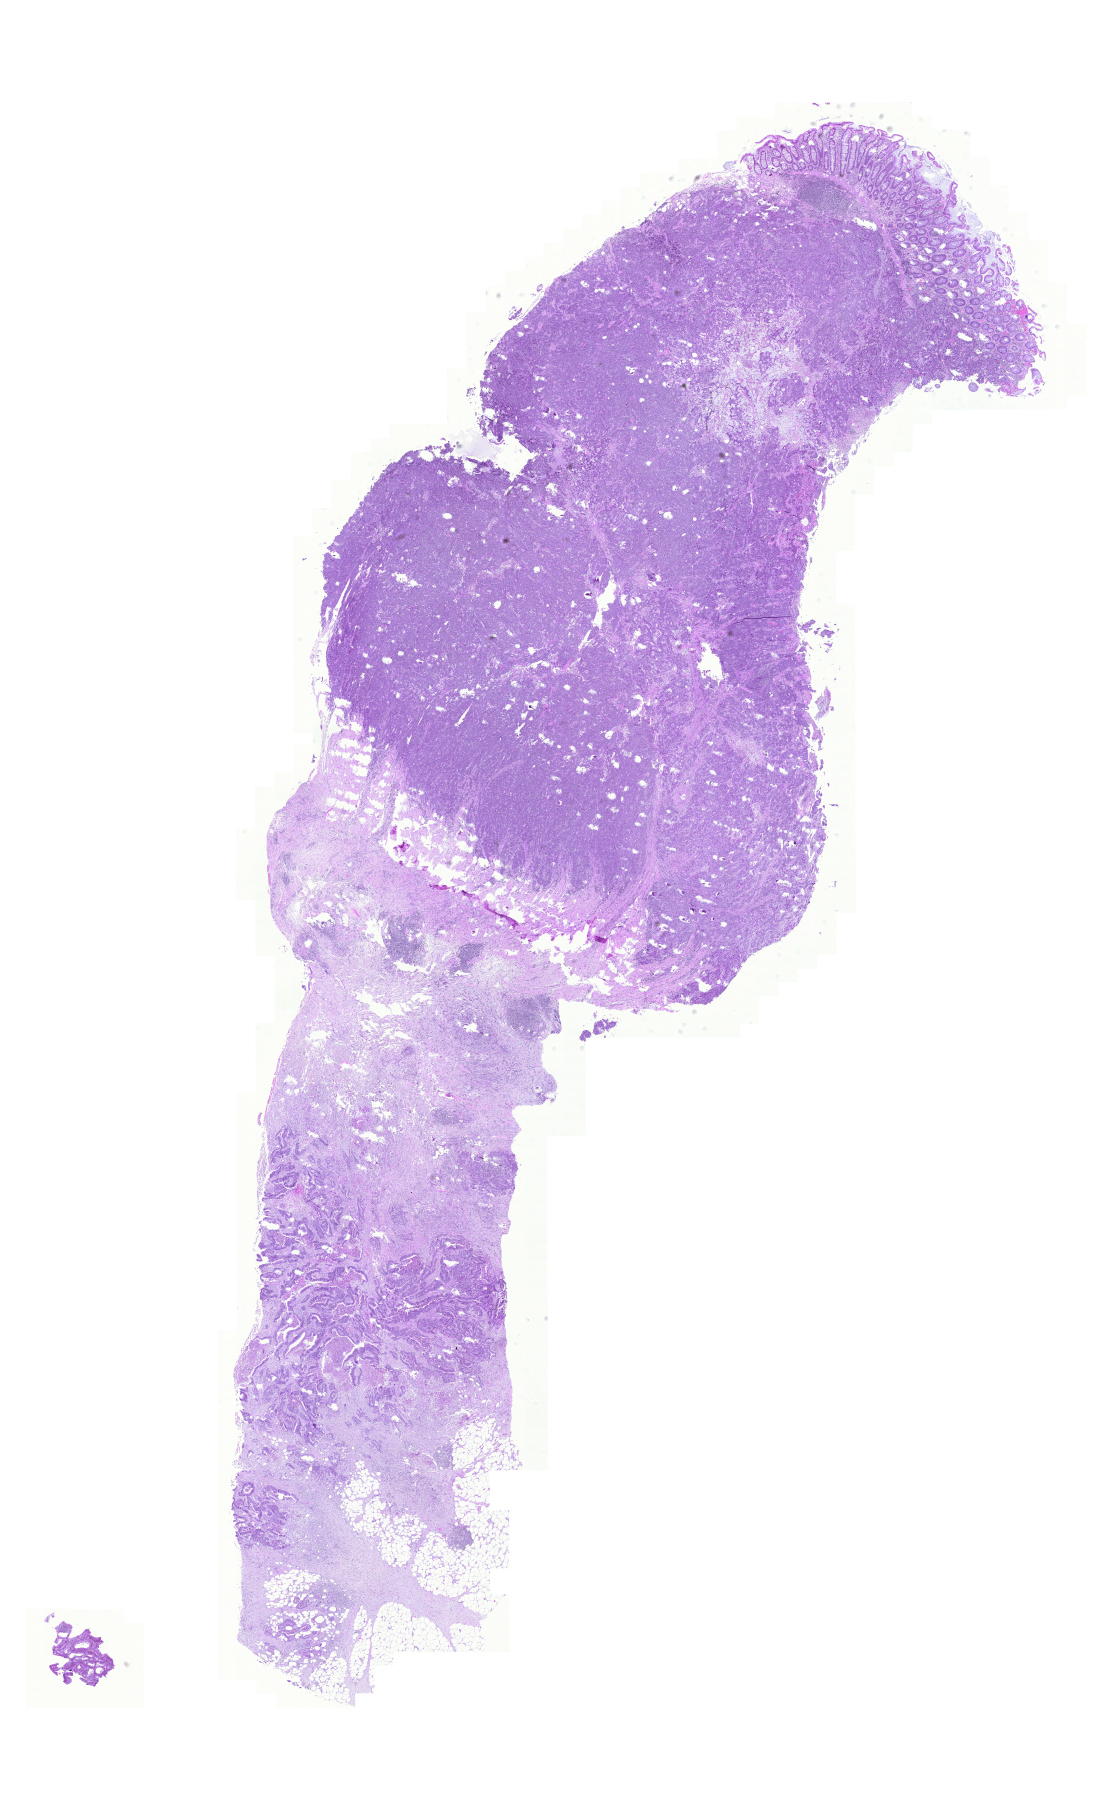
H&E-stained whole-slide image — a low-resolution overview of the entire scanned area, about 16.3 x 26.7 mm (slide scanned at 20x), formalin-fixed paraffin-embedded (FFPE) diagnostic section, colon, primary tumour sample. Male patient; age at initial diagnosis 47 years.
Diagnosis: Mucinous adenocarcinoma (ascending colon). AJCC pathologic stage: III (5th edition).